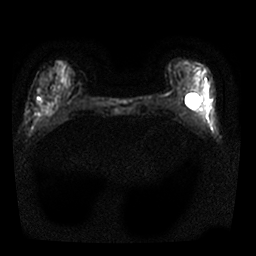
Breast MRI, one axial slice. Slice 9 of 25 in the series (ordered by position). Diffusion-weighted series; image 2 of 4 stored at this slice position (different b-values; order by instance number). 1.5 T. 4 mm slice thickness. 256 × 256 image matrix, field of view 310 × 310 mm. Female patient.
Annotated regions visible in this slice (manually delineated by an expert):
- tumour on diffusion-weighted imaging: bounding box [x1, y1, x2, y2] px = [37, 88, 41, 93]